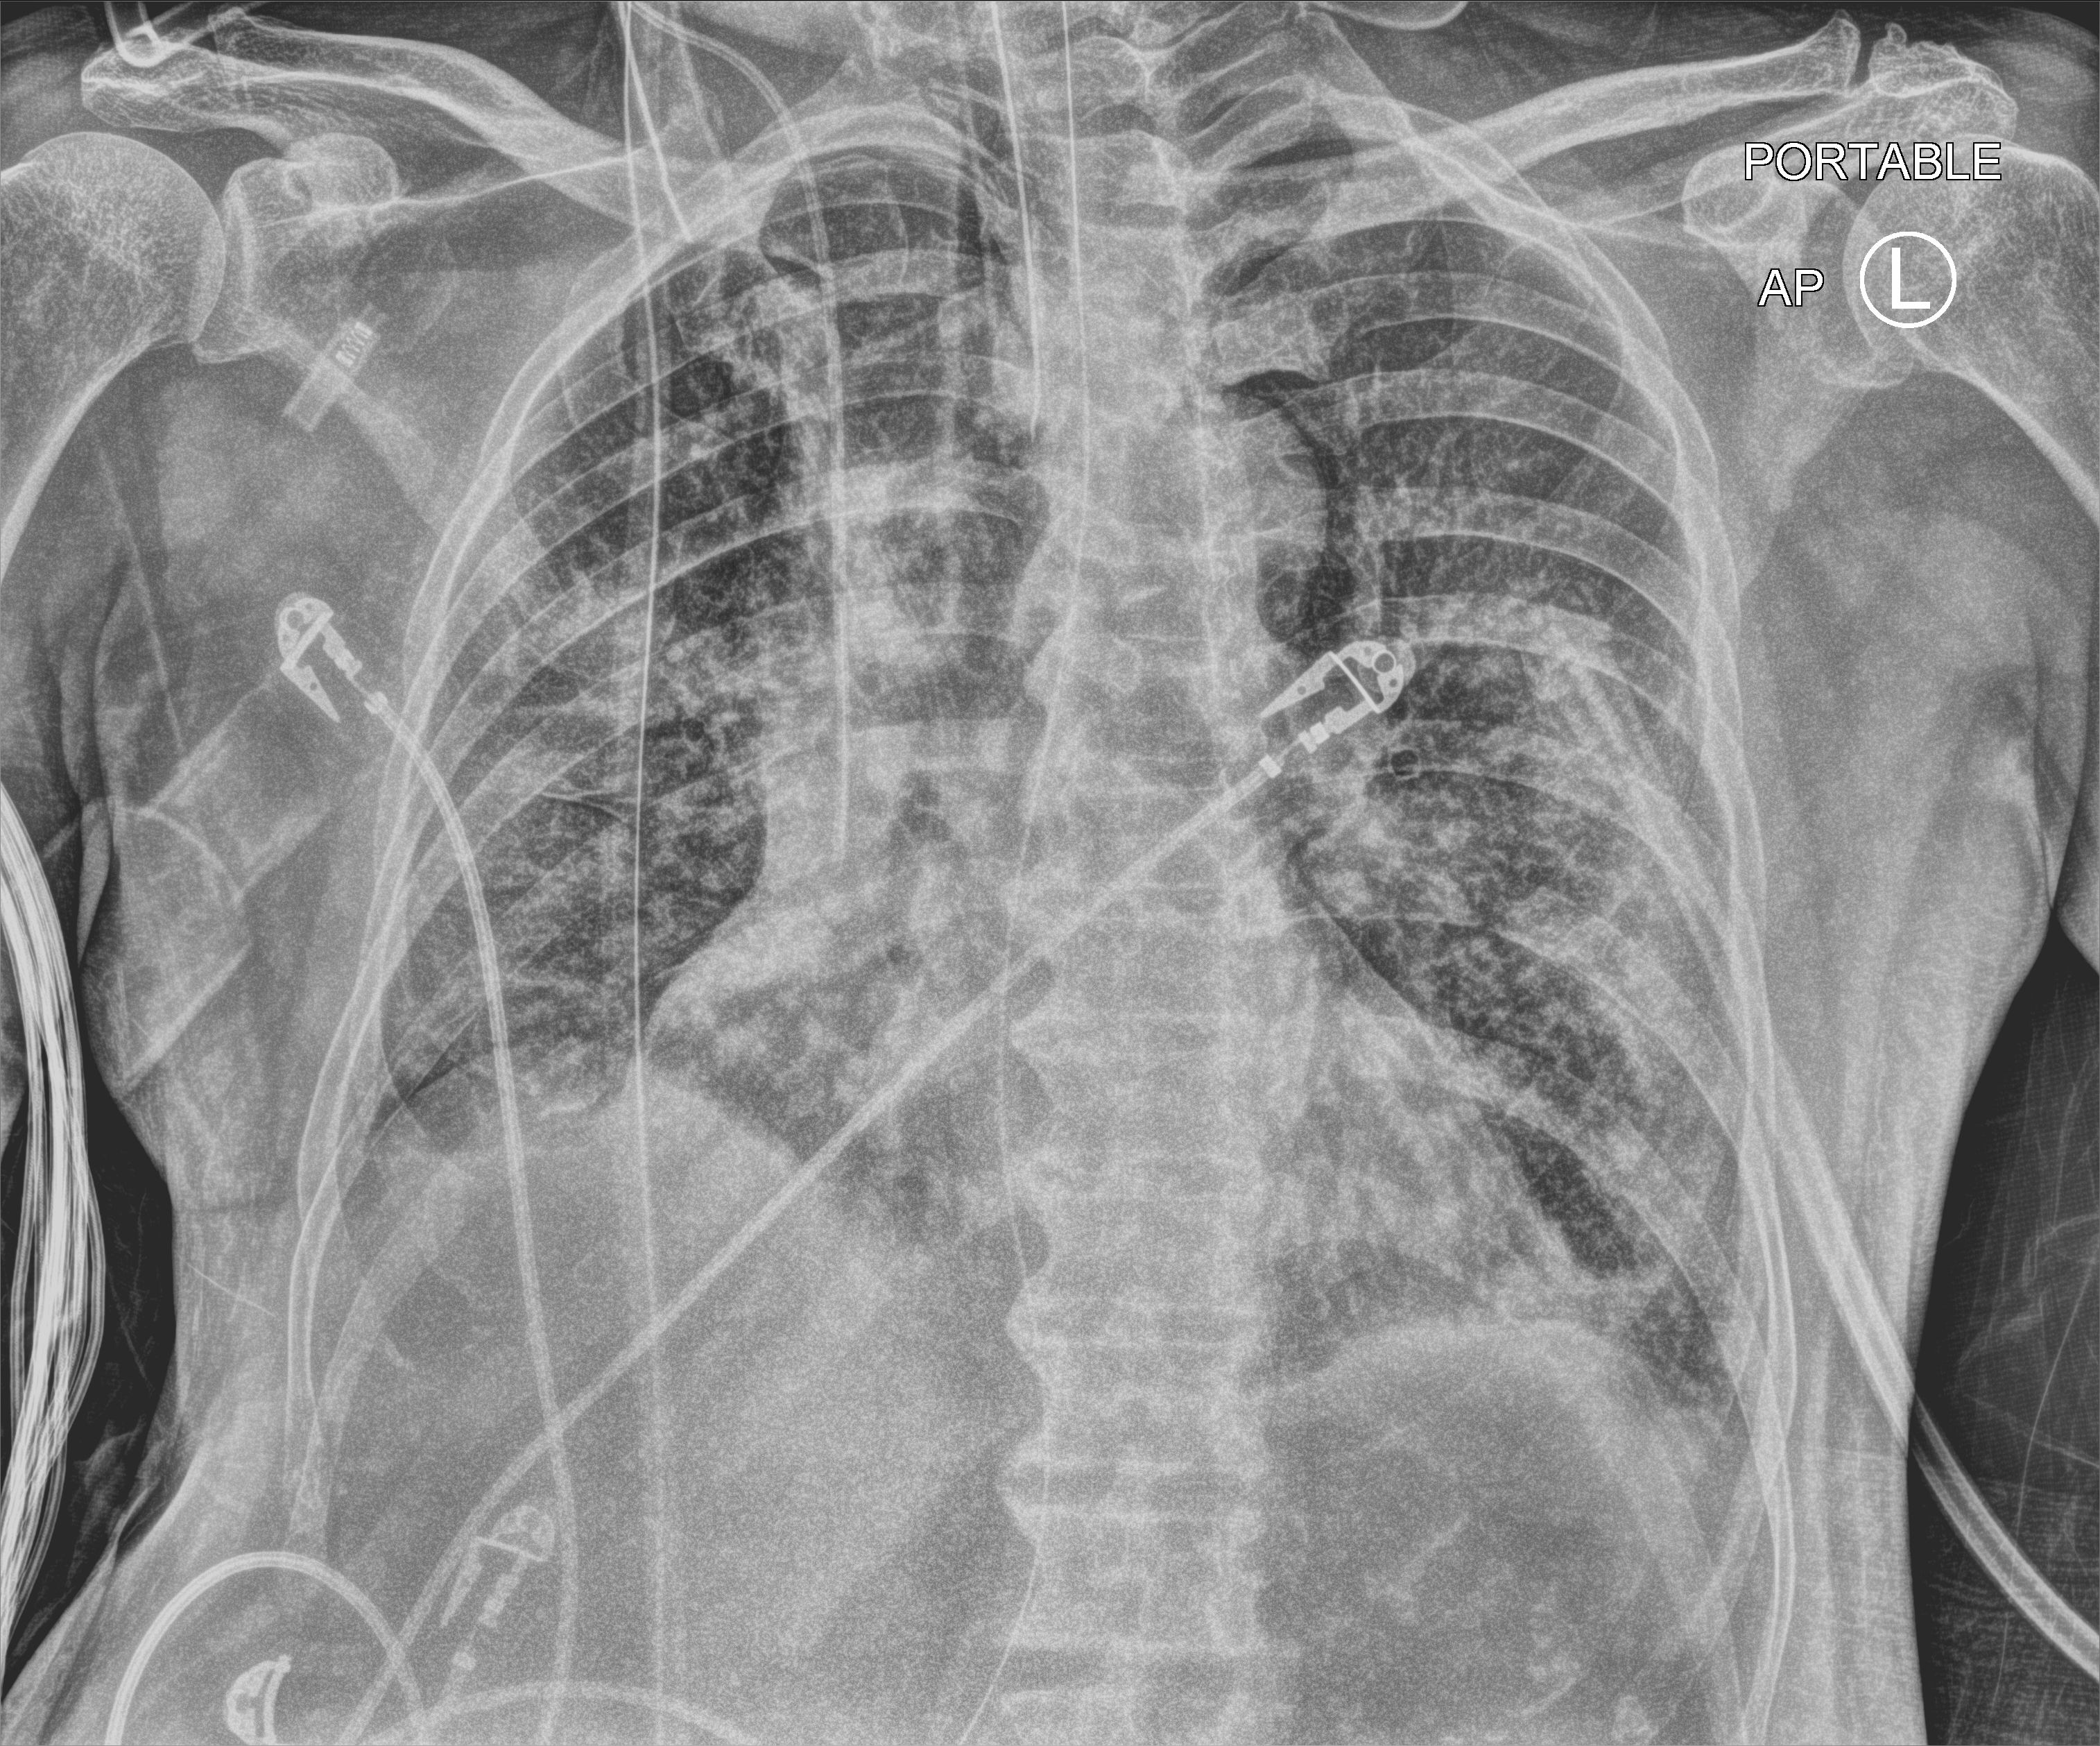
Chest X-ray (portable). Male patient hospitalised with COVID-19, age 60–74 years.
Hospital-stay facts (about this admission, not read from this image; timing relative to this image not recorded): admitted to intensive care during this hospital stay: yes; mechanically ventilated during this hospital stay: yes.